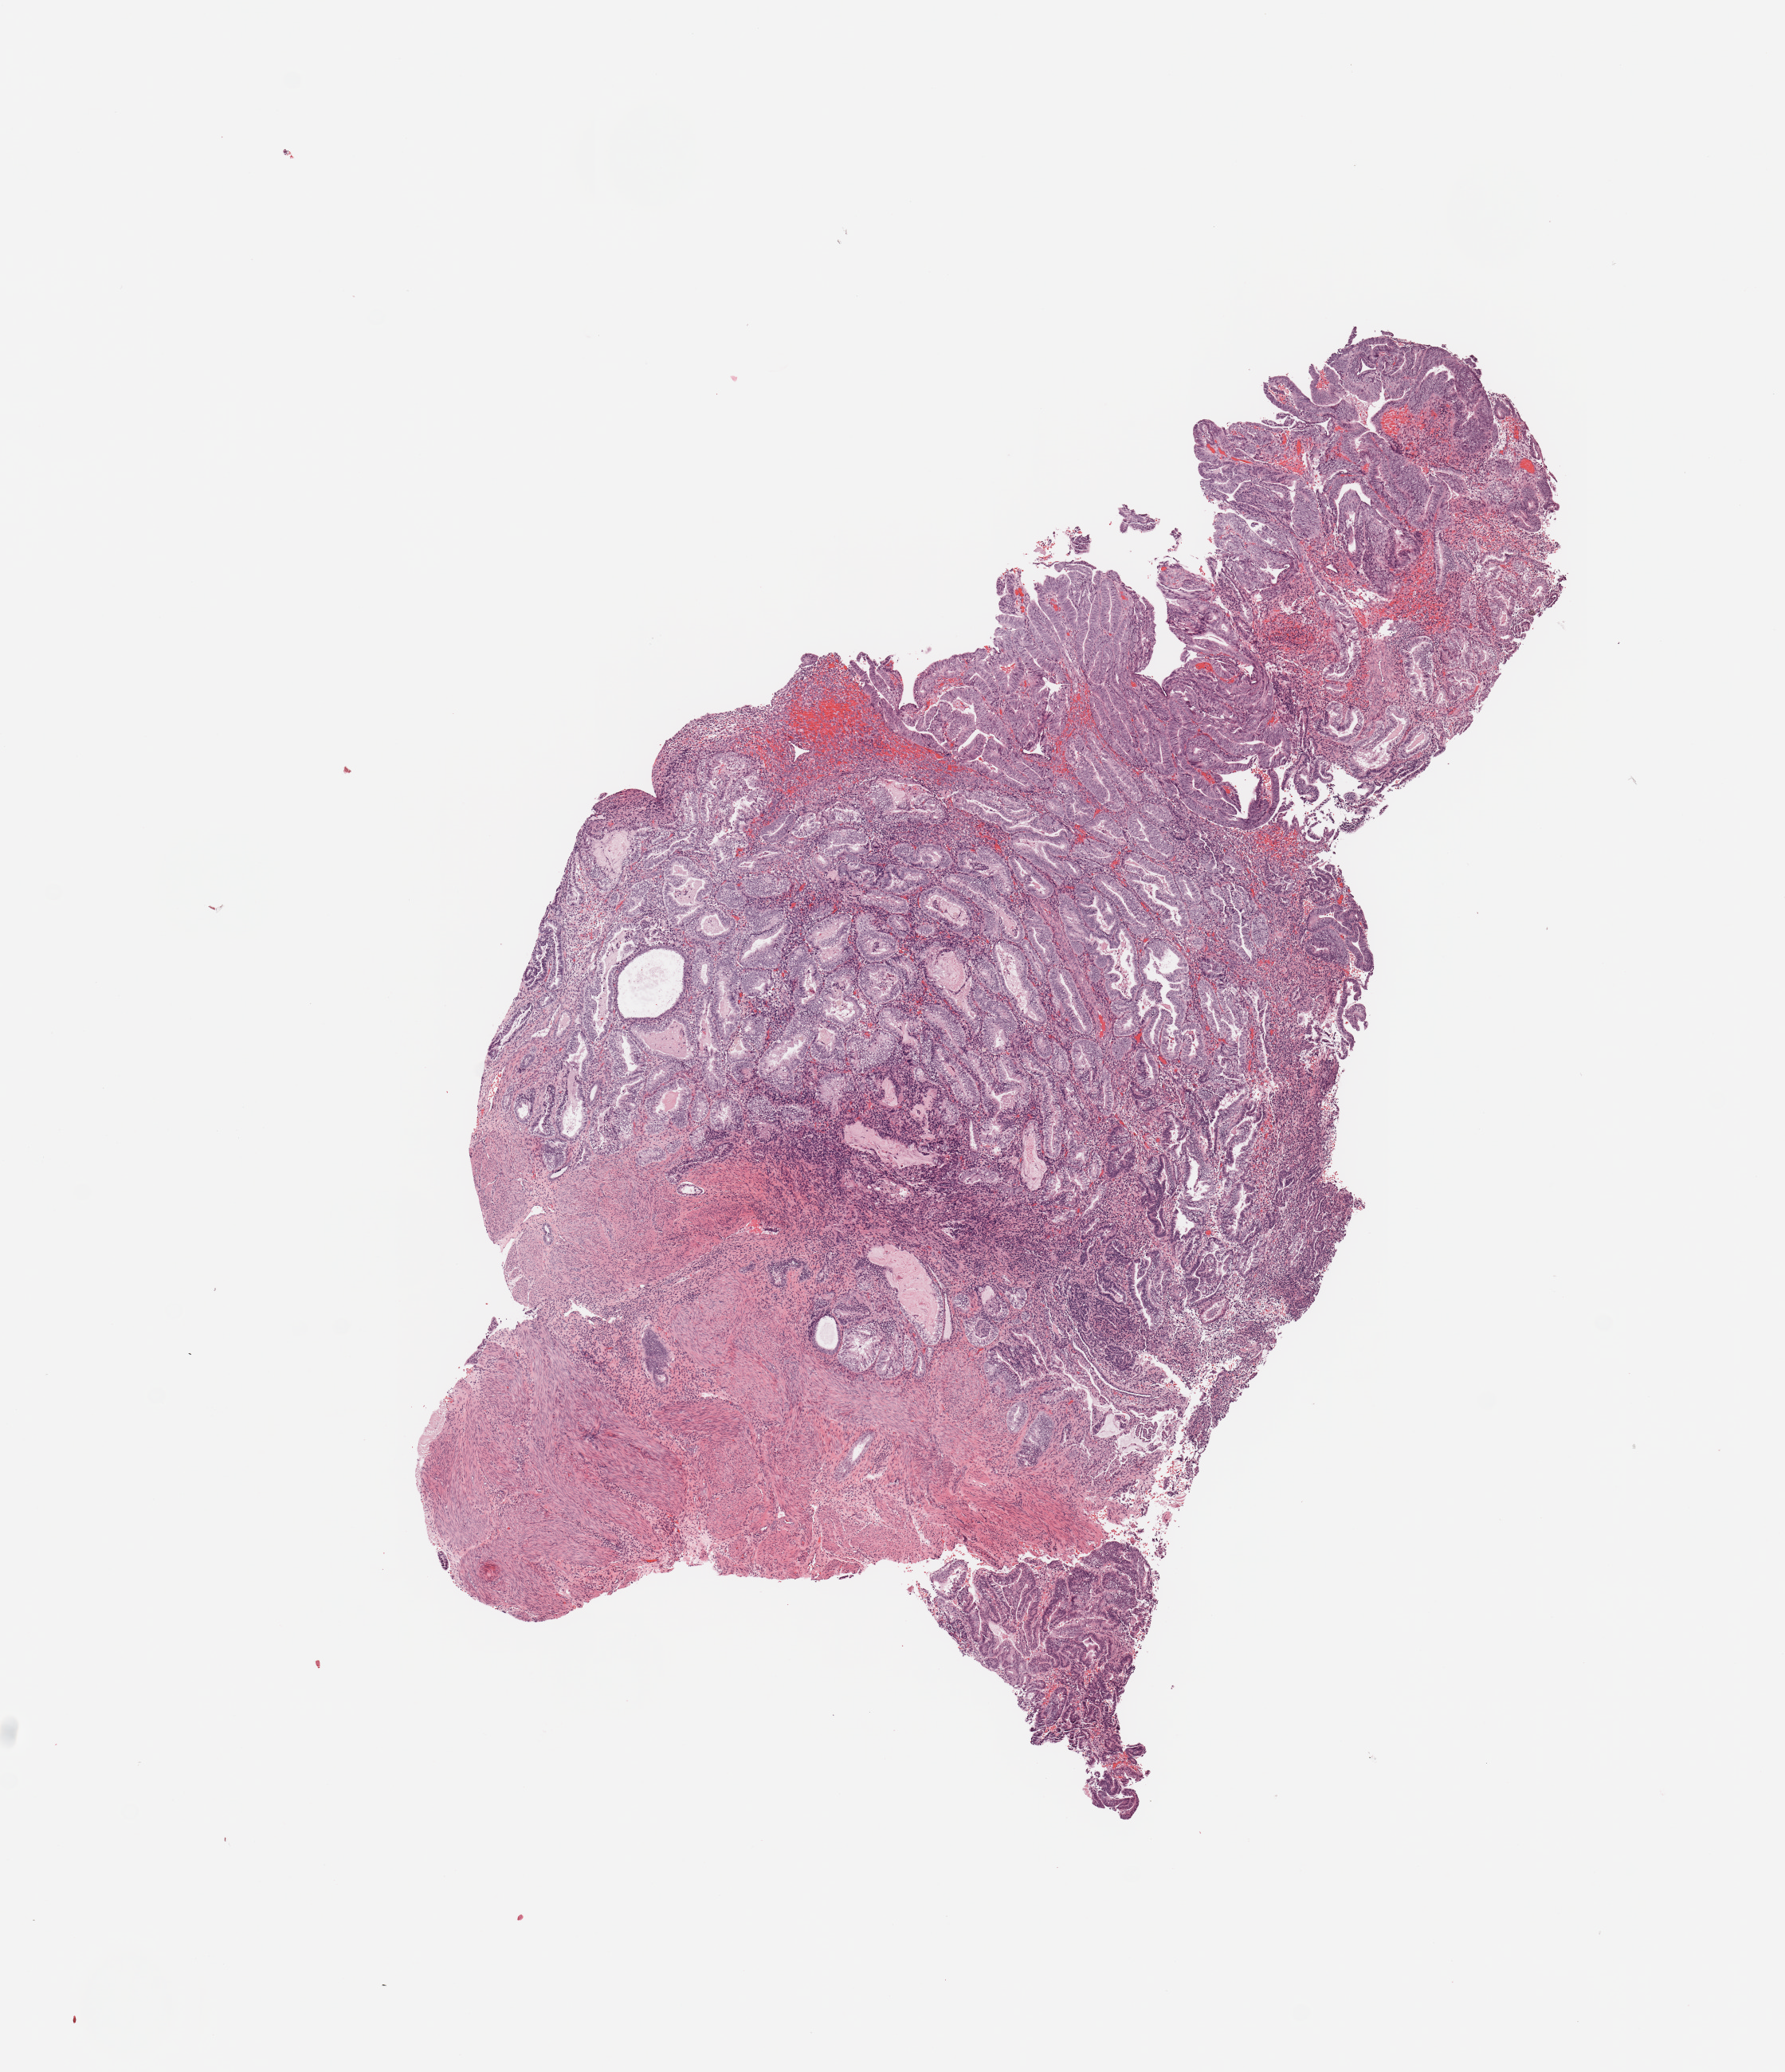
Hematoxylin and eosin (H&E) stained whole-slide image — whole scanned area (about 8.9 x 10.3 mm, slide scanned at 20x) shown as a low-resolution overview, tumour tissue sample, sampled site: uterus. Female, 67 y/o. Pathologist review of this section (percent, as recorded): tumour nuclei 80%, necrosis 2%.
Diagnosis: Endometrioid adenocarcinoma, NOS.